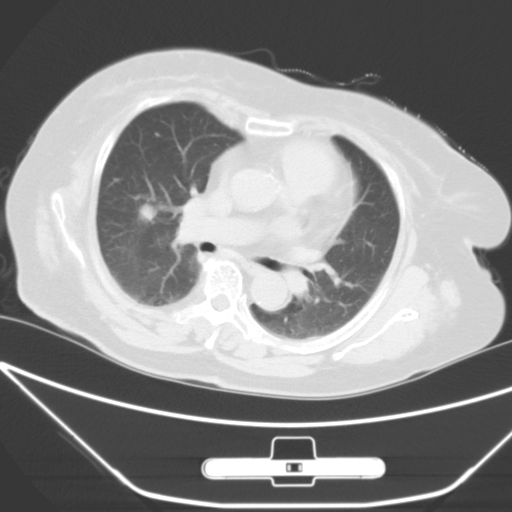
Chest CT, one axial slice. Position 31 of 49 along the scan axis. 120 kVp. Lung window (W 1500 / L -600 HU). 5 mm slice thickness. 512 × 512 image matrix. Patient: female, 65 years. From the clinical record (not read from this slice): clinical TNM (as recorded): T1c N0 M0; histopathological grade: G3.
Outlined on this slice (bounding box drawn by a radiologist):
- lung tumour (recorded histology: adenocarcinoma): box from (x=139, y=195) to (x=164, y=231) px